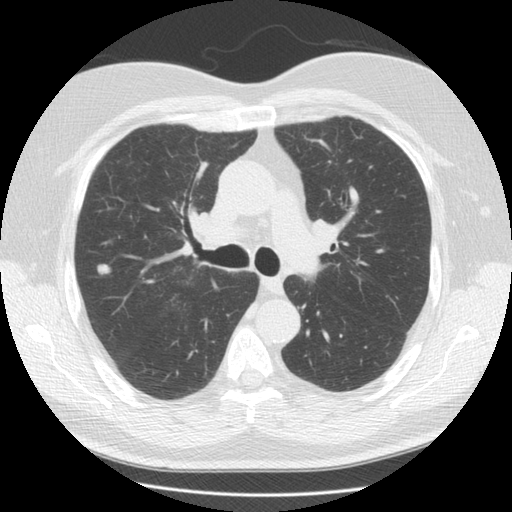
Axial slice from a low-dose chest CT screening exam, third annual screen, lung window (W 1500 / L -600 HU), 2.5 mm slice thickness, standard (soft-tissue) reconstruction kernel (STANDARD), 120 kVp, slice 55 of 146 in the series. Male, age 65 years at enrolment.
Lesion marked by an expert reader, bounding box <91,257,118,284> (left, top, right, bottom; pixels). Reader record for this screening exam (exam-level; its link to the box is not recorded): non-calcified nodule or mass ≥4 mm, right upper lobe, 12 × 12 mm, smooth margins, soft tissue attenuation, pre-existing on the prior screen: yes; interval growth: yes. Lung cancer was diagnosed 54 days after this screen: adenocarcinoma, NOS, right upper lobe, poorly differentiated (G3), stage IA (AJCC 6th edition), 17 mm at pathology.